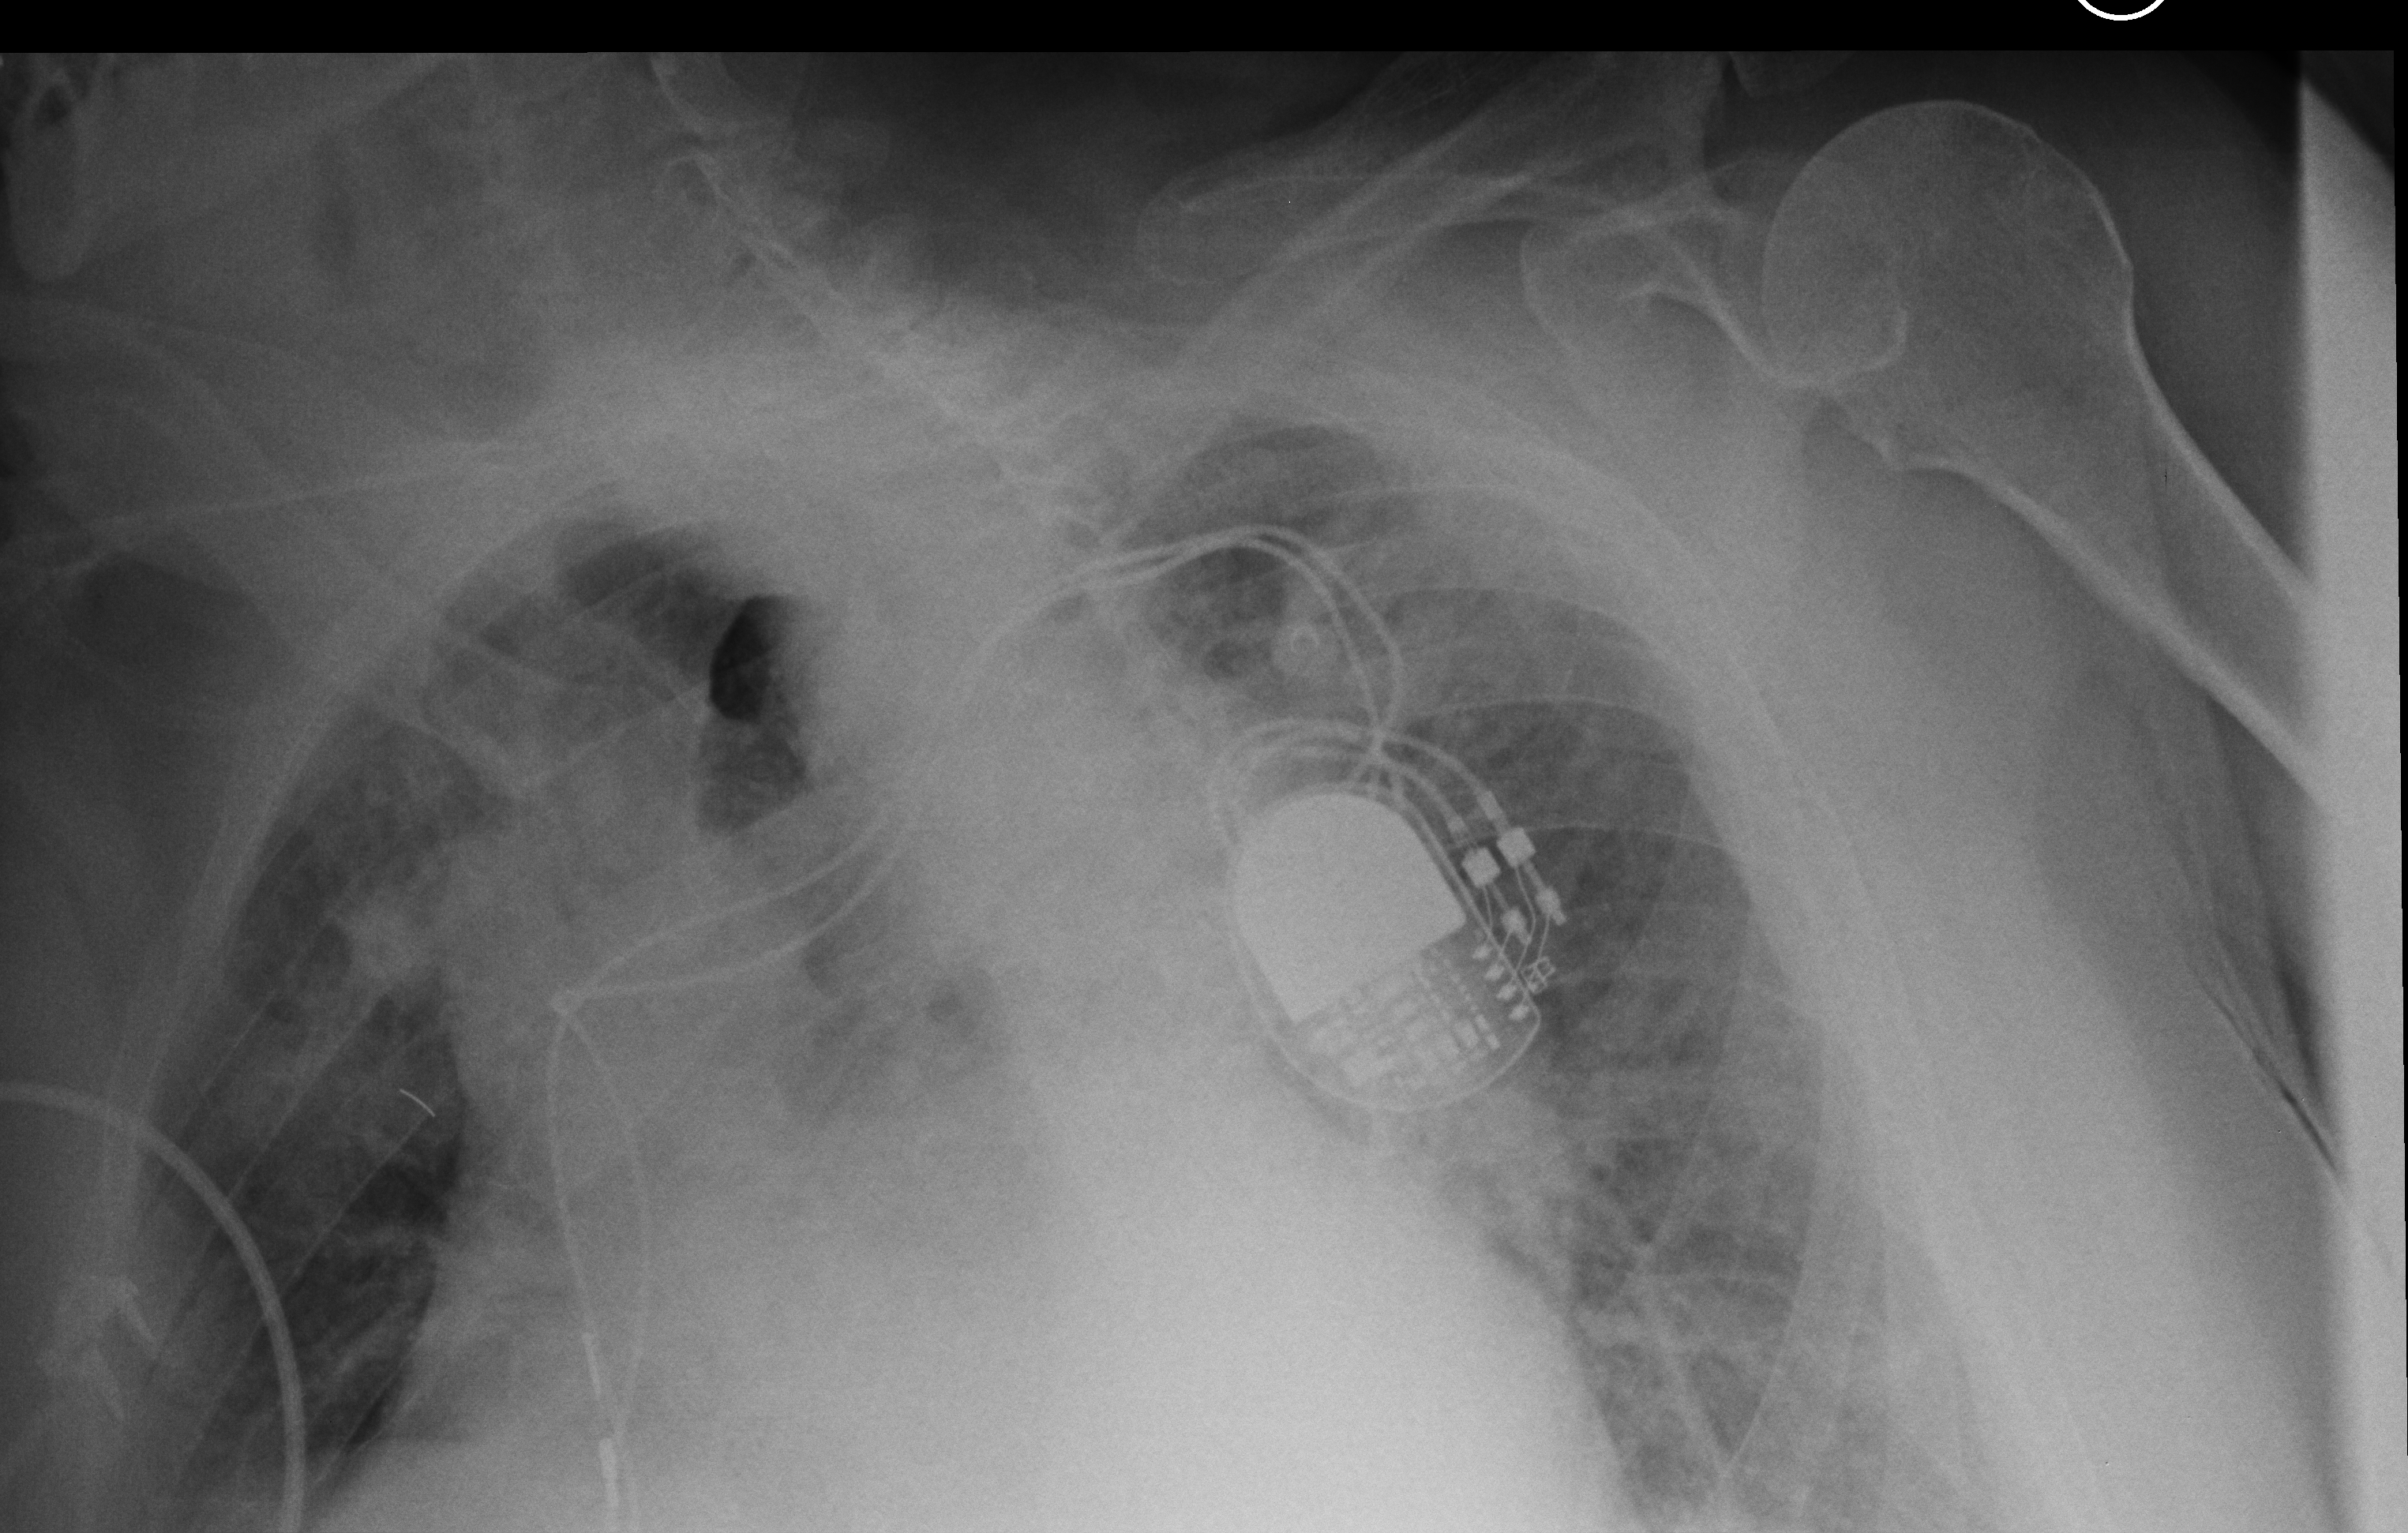
Chest X-ray (portable), anteroposterior (AP) projection. Patient hospitalised with COVID-19; male, aged 75–90 years.
Hospital-stay facts (about this admission, not read from this image; timing relative to this image not recorded): mechanically ventilated during this hospital stay: no; admitted to intensive care during this hospital stay: no.